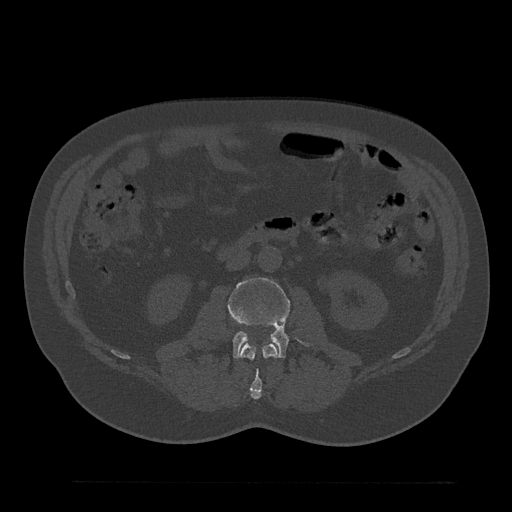
CT including the spine, one axial slice. Position 61 of 797 along the scan axis. Reconstruction kernel Br40s/3. 120 kVp. Bone window (W 1800 / L 400 HU). 0.5 mm slice thickness. 512 × 512 image matrix, field of view 430 × 430 mm. Male patient, age 61 years. Case-level facts recorded for this patient, not image findings: primary cancer: prostate.
Annotated regions visible in this slice (semi-automatically segmented with operator editing):
- L2 vertebra: box from (x=240, y=344) to (x=278, y=399) px
- L3 vertebra: (x=228, y=277)–(x=308, y=358)